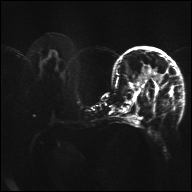
Breast MRI, one axial slice. Position 16 of 32 along the scan axis. Diffusion-weighted series; image 2 of 4 stored at this slice position (different b-values; order by instance number). 1.5 T. 4 mm slice thickness. 192 × 192 image matrix, field of view 360 × 360 mm. Female patient.
Annotated regions visible in this slice (manually delineated by an expert):
- tumour on diffusion-weighted imaging: box from (x=149, y=68) to (x=164, y=78) px